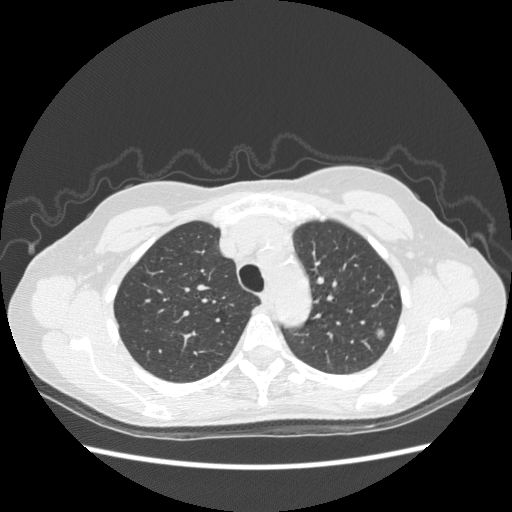
Axial slice from a low-dose chest CT screening exam, first (baseline) screen, lung window (W 1500 / L -600 HU), standard (soft-tissue) reconstruction kernel (STANDARD). Female participant, aged 61 years at enrolment. Former smoker at enrolment.
• Expert reader's lesion annotation, bounding box <357,320,392,351> (left, top, right, bottom; pixels).
• The exam's reader record, not a measurement of the box and not confirmed to be the same lesion: non-calcified nodule or mass ≥4 mm, left upper lobe, 7 × 6 mm, poorly defined margins, ground glass attenuation.
• Participant outcome: lung cancer diagnosed 484 days after this screen — bronchiolo-alveolar adenocarcinoma, NOS, left upper lobe, well differentiated (G1), stage IA (AJCC 6th edition), 8 mm at pathology.